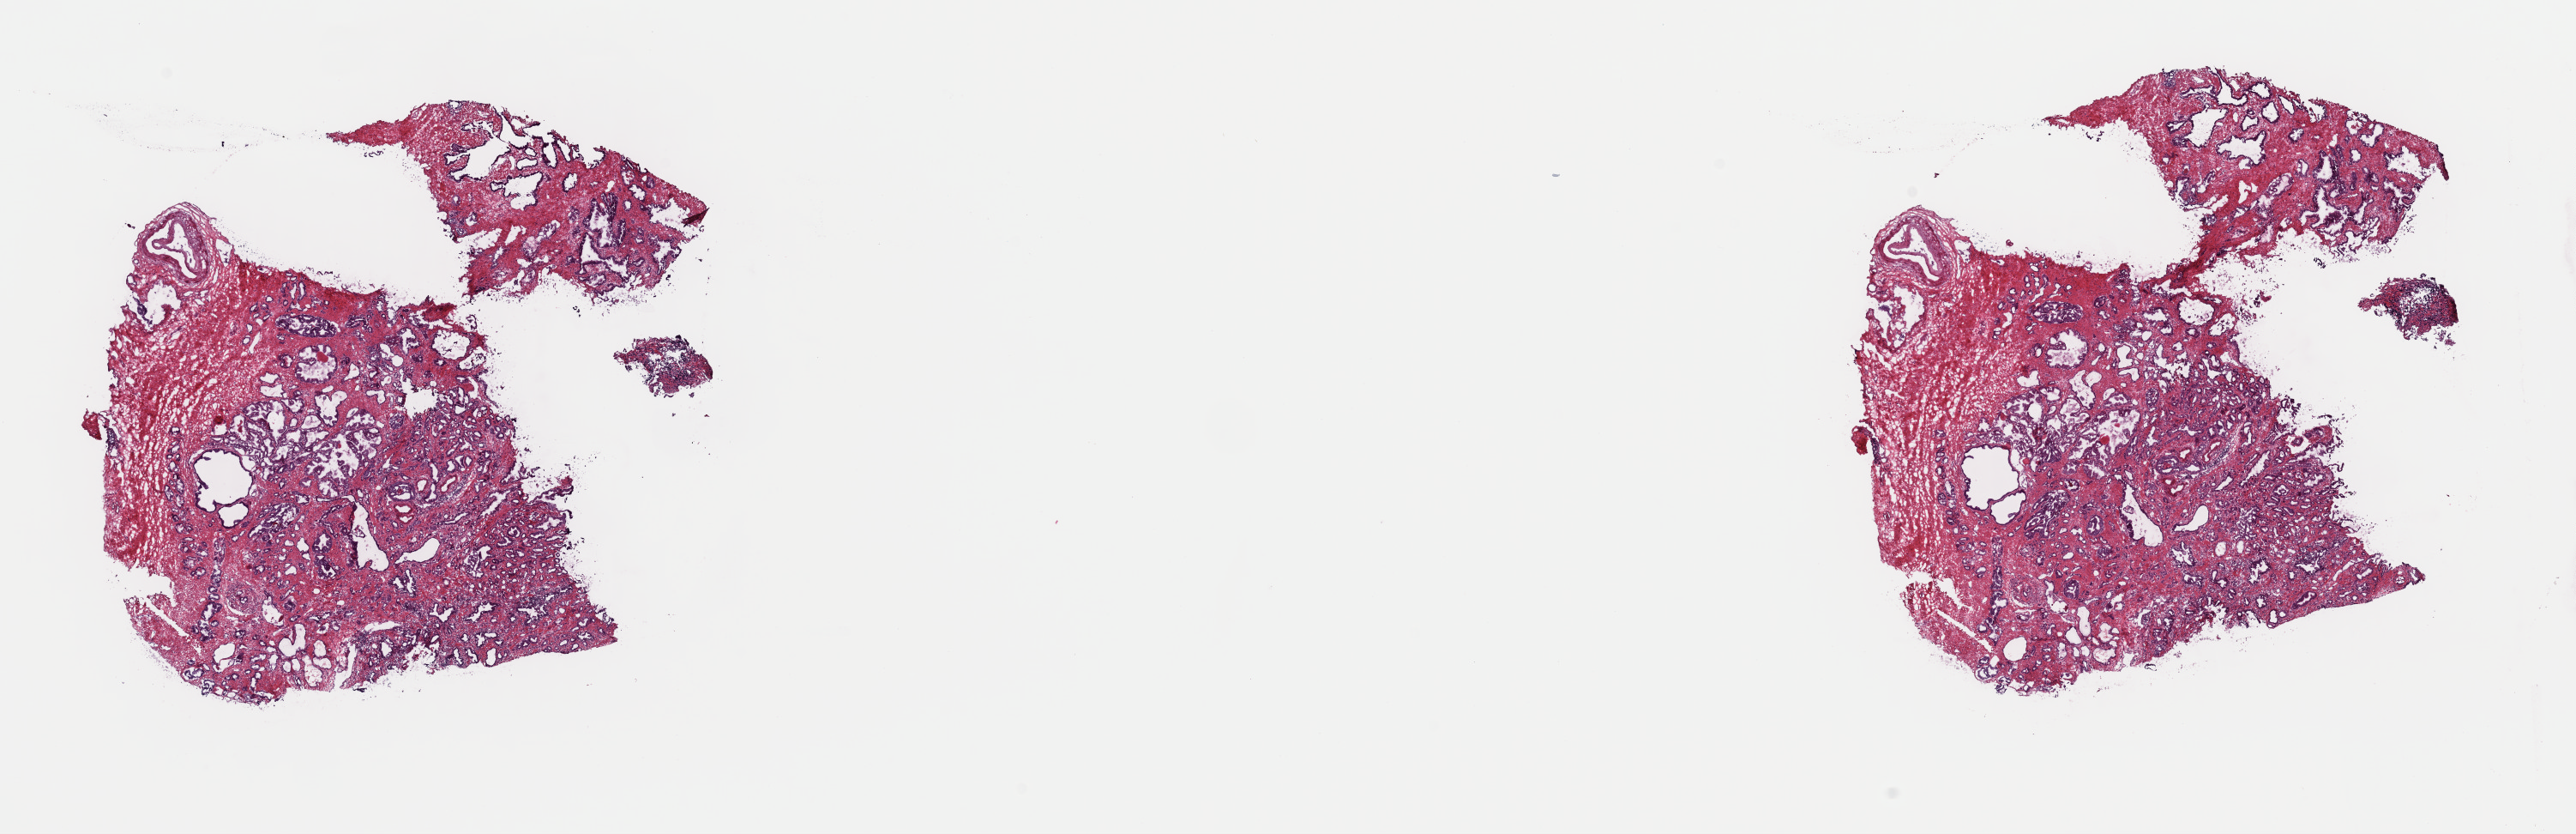
Digitized Hematoxylin and eosin (H&E) stained tissue section (whole slide), low-resolution overview of the scanned area, about 23.7 x 7.7 mm (acquisition: 40x scan), frozen section from the top of the tissue portion, primary tumour sample from the prostate. Patient: male, age at initial diagnosis 65 years.
Pathologic diagnosis: Adenocarcinoma, NOS (prostate gland).